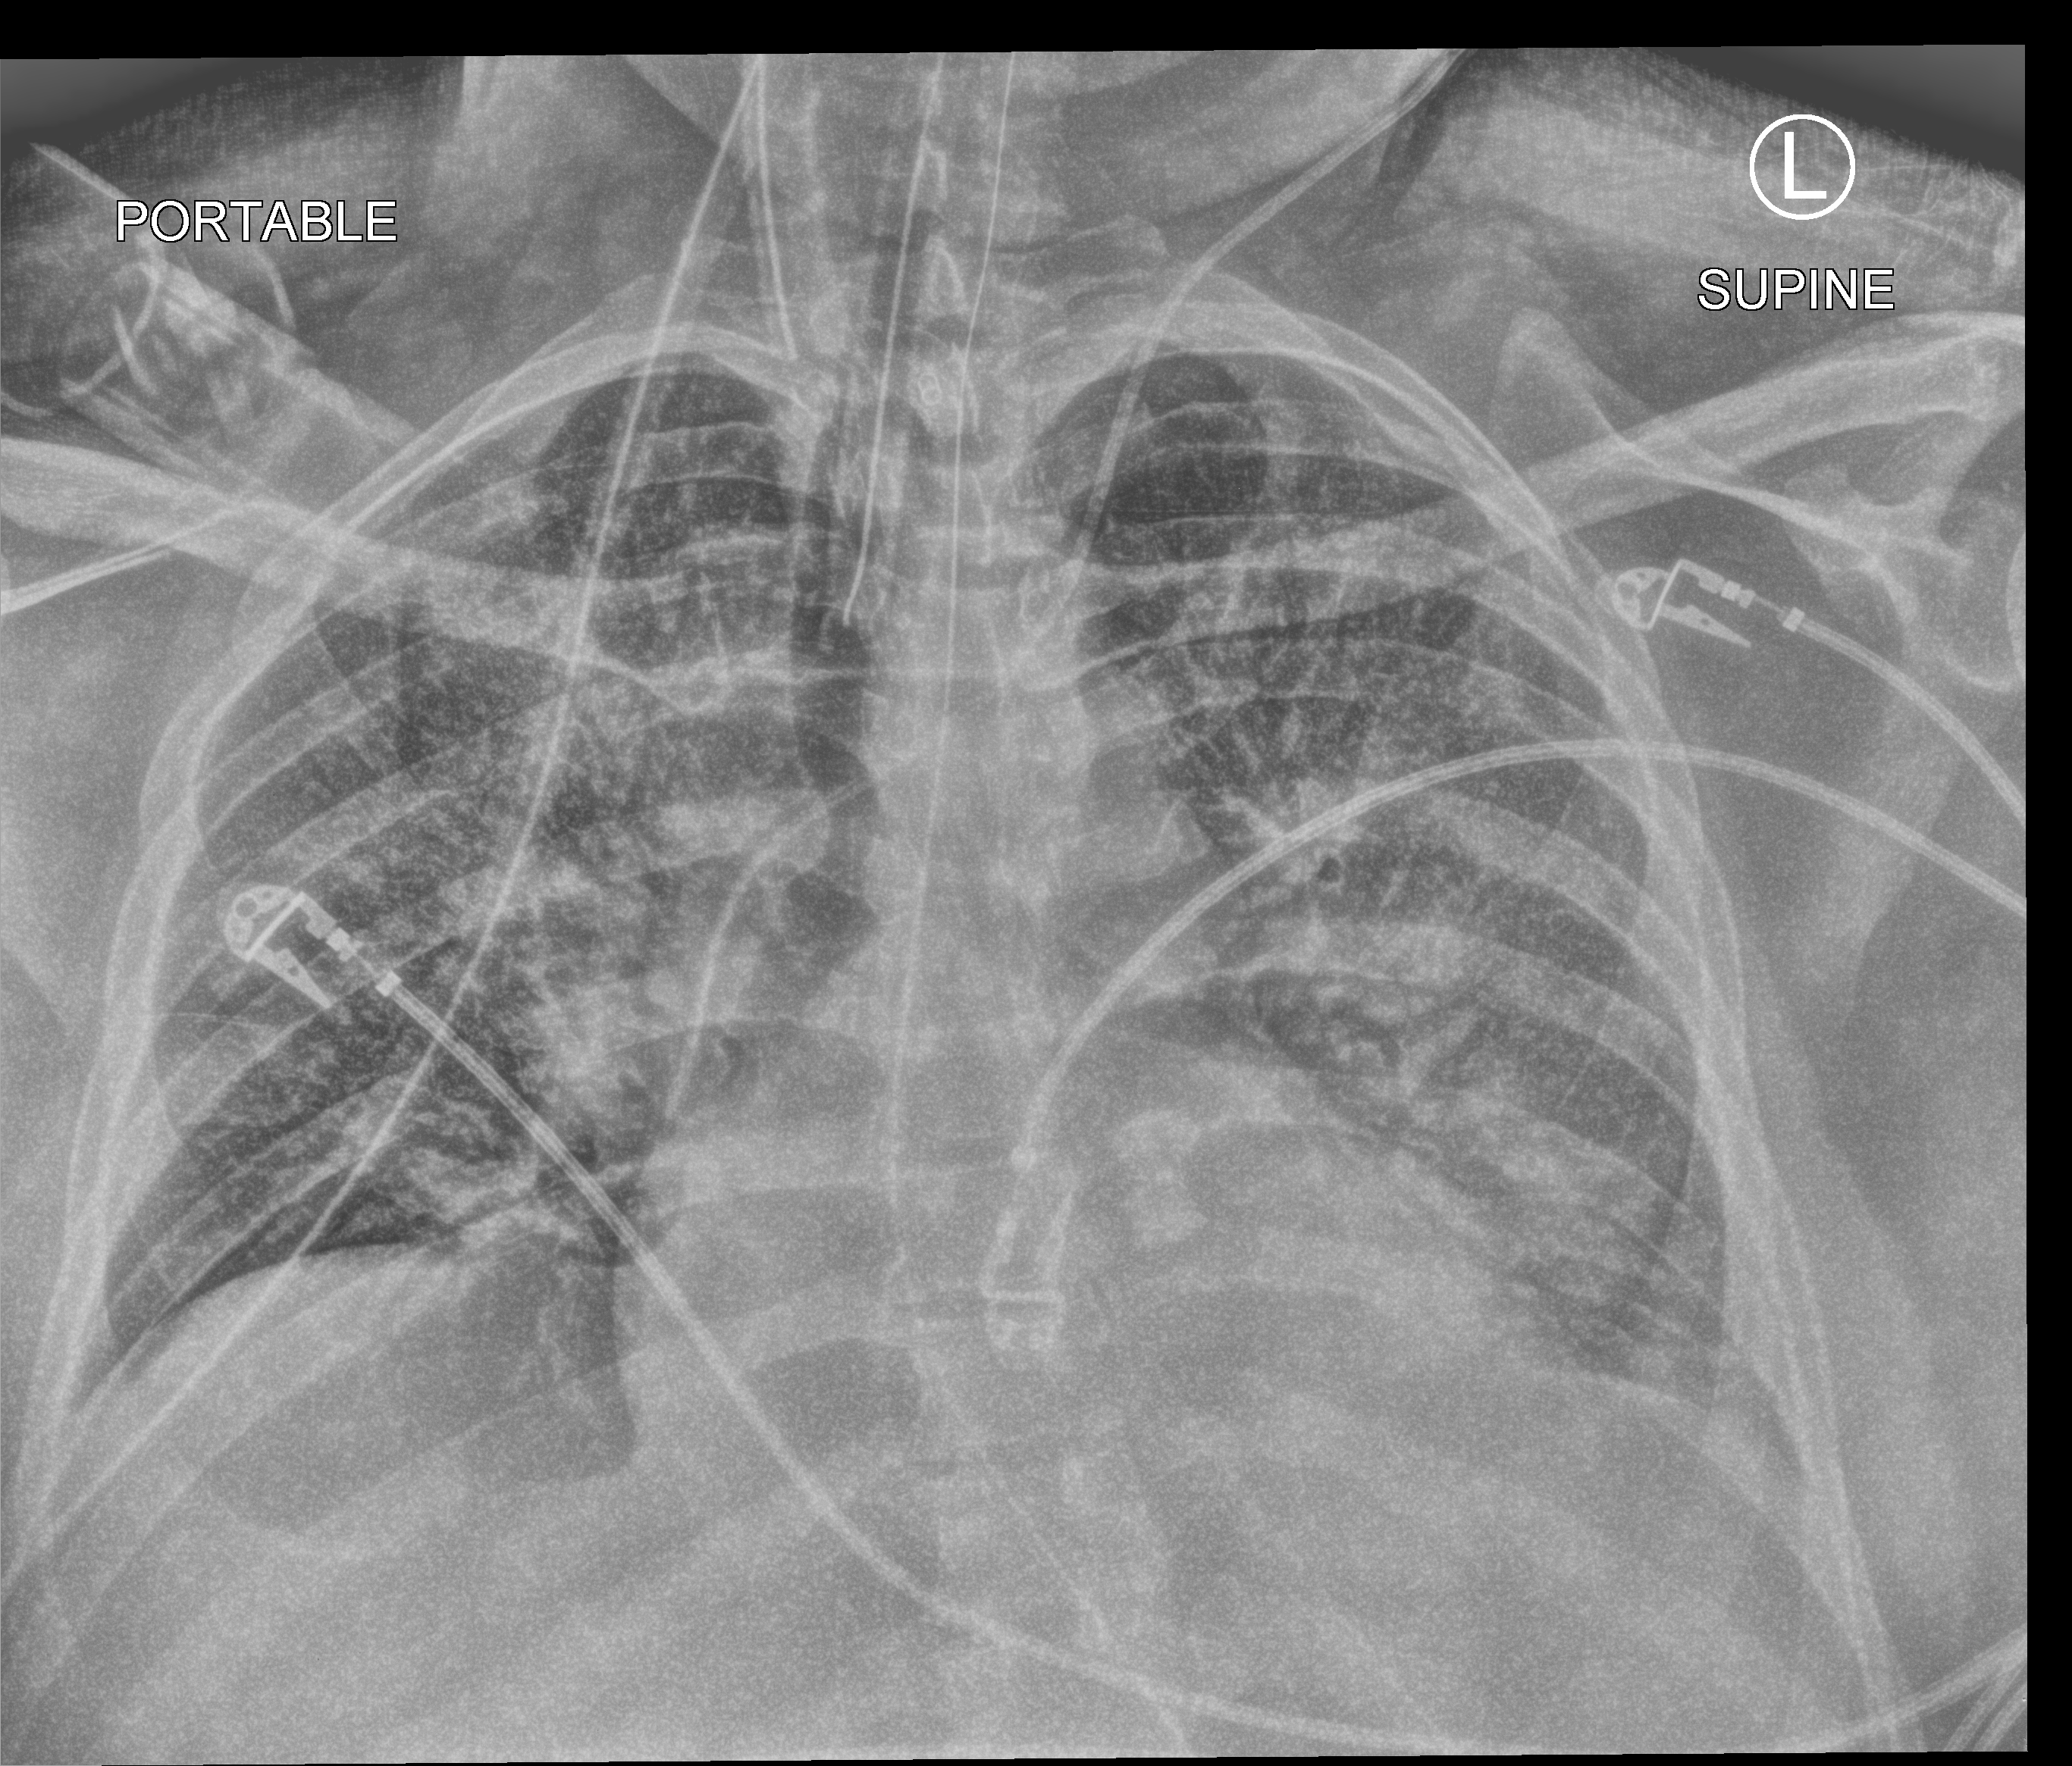
Bedside chest radiograph (computed radiography). Adult patient hospitalised with COVID-19, age 18–59 years.
Admission-level facts for this patient (not findings on this image; timing relative to this image not recorded):
- admitted to intensive care during this hospital stay: yes
- chronic kidney disease (admission record): no
- mechanically ventilated during this hospital stay: yes